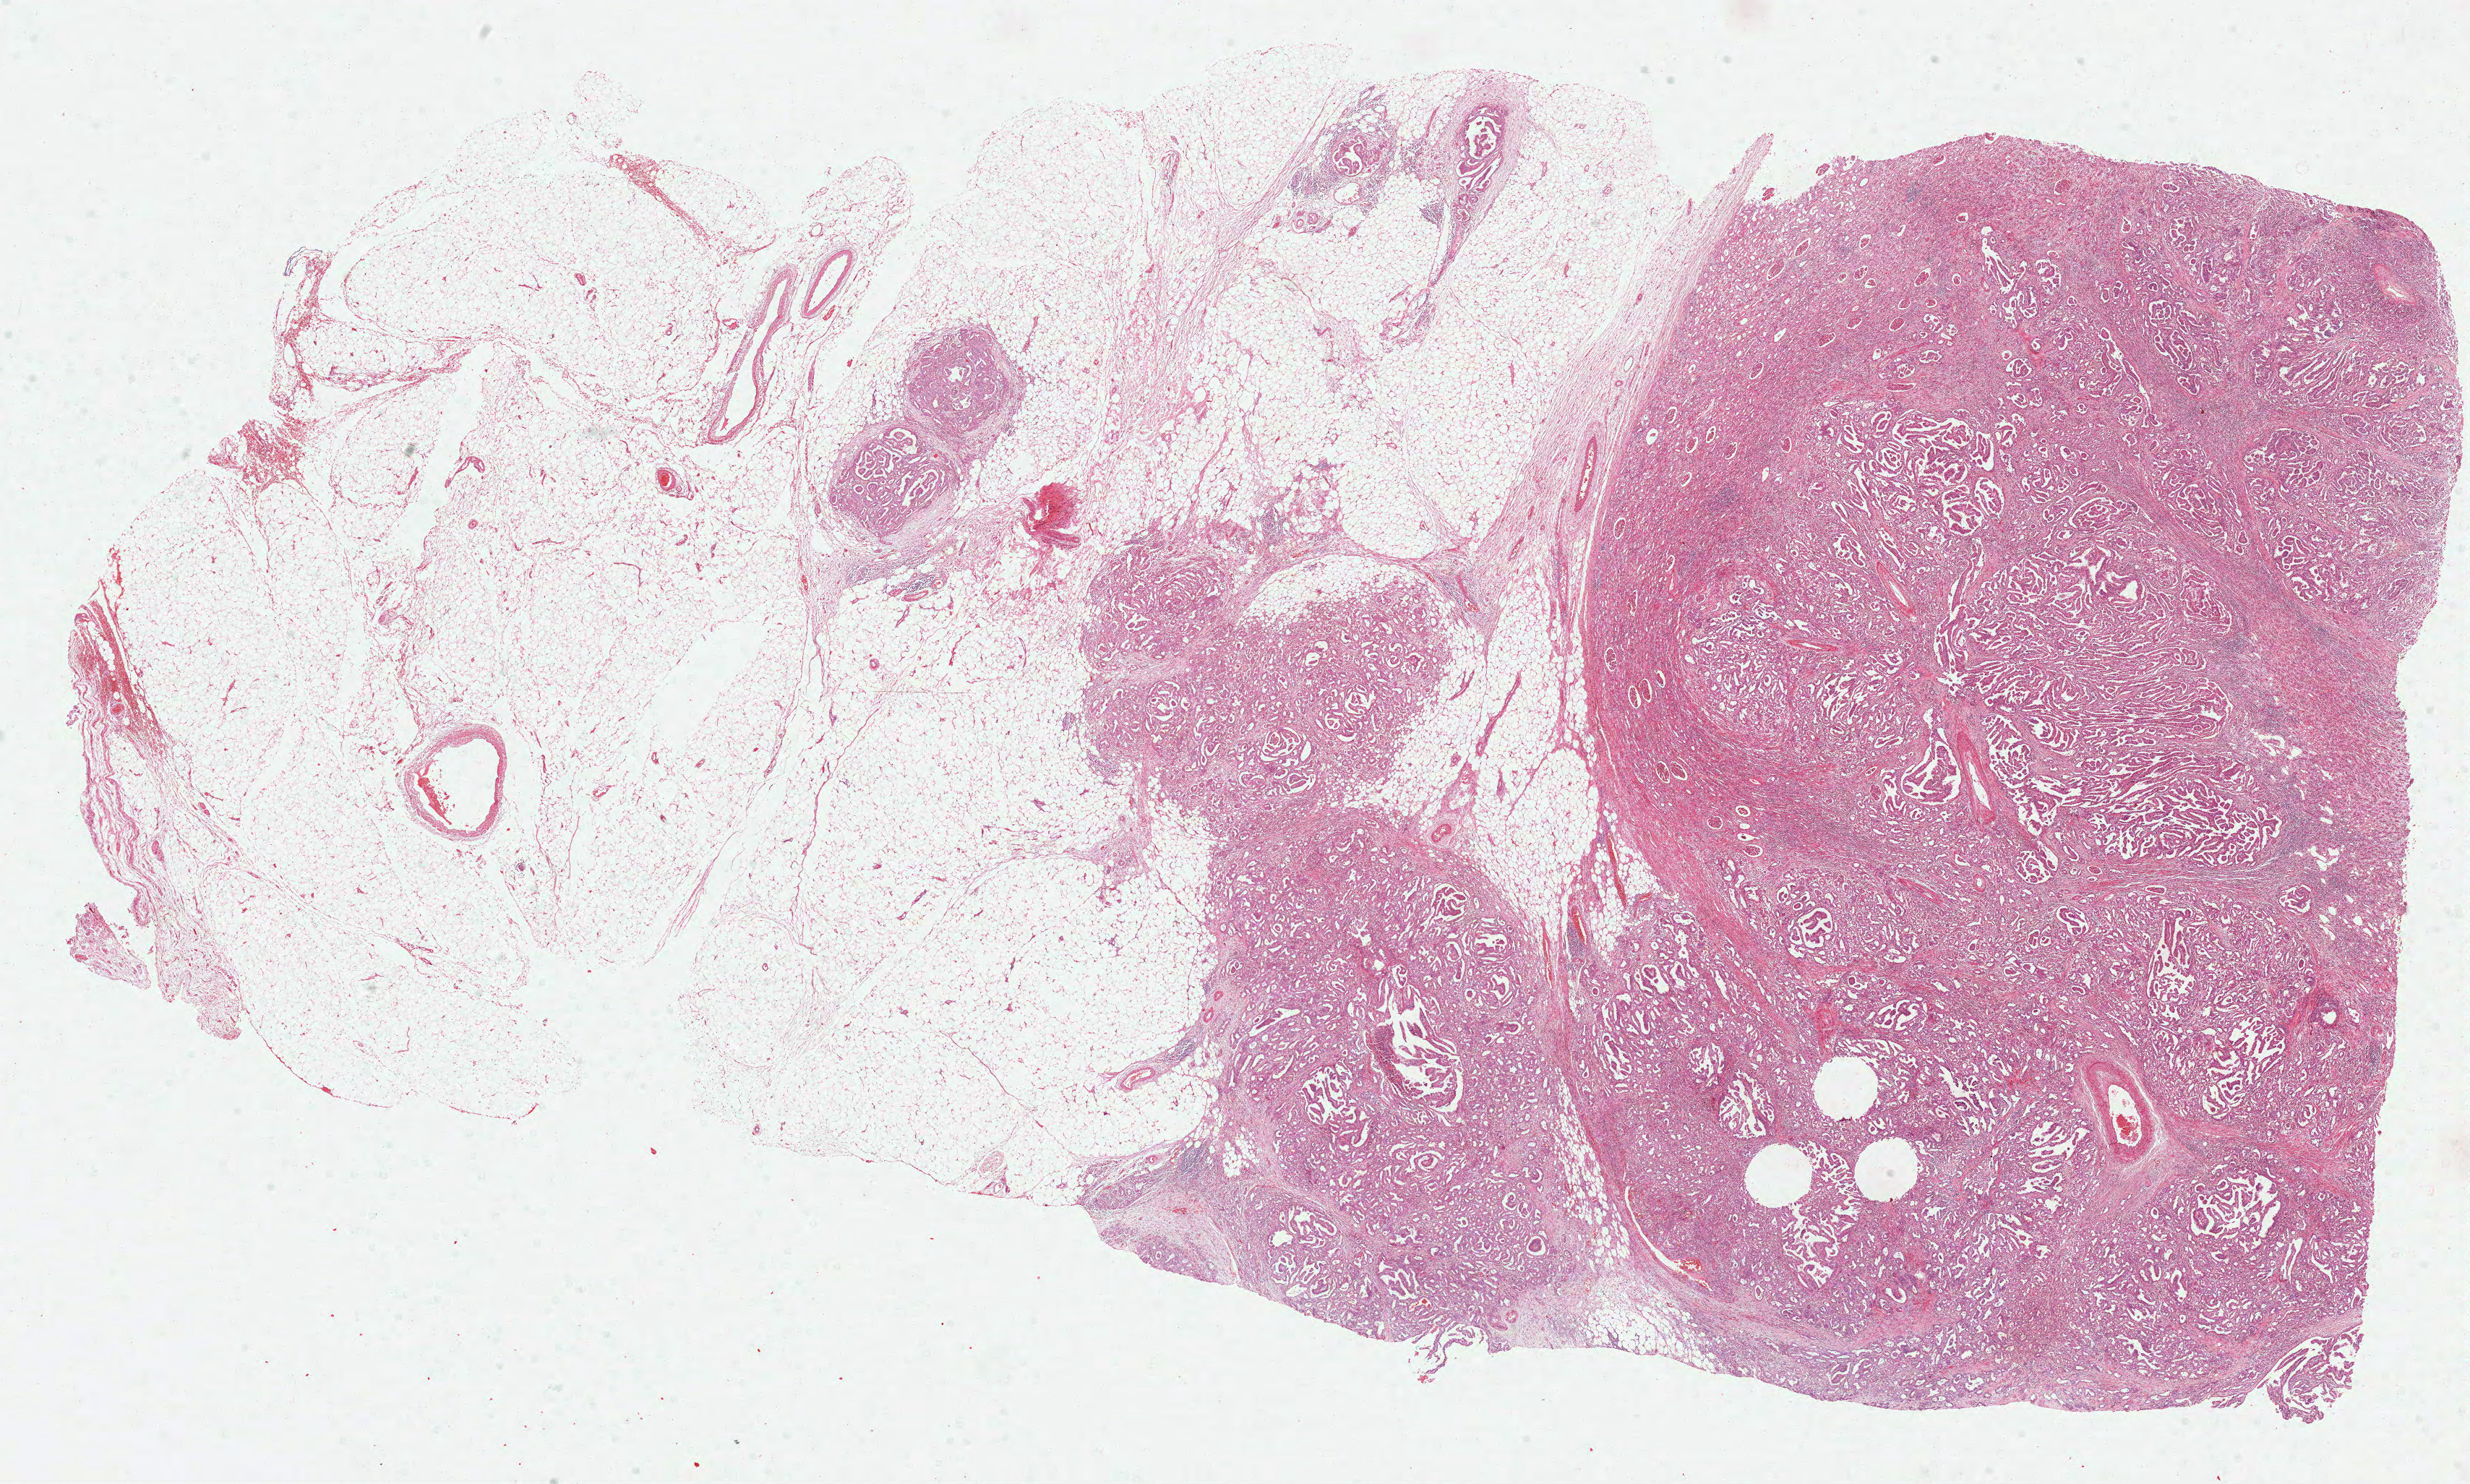
Hematoxylin and eosin (H&E) stained whole-slide image, whole scanned area (about 27.6 x 16.6 mm, from a 40x scan) shown as a low-resolution overview. Formalin-fixed paraffin-embedded (FFPE) diagnostic section. Primary tumour sample from the kidney. Female patient; age at initial diagnosis 53 years.
Laterality: left. AJCC pathologic stage: IV (6th edition). Lymph nodes positive (case pathology): 4 of 4 examined. Pathologic diagnosis: Papillary adenocarcinoma, NOS.